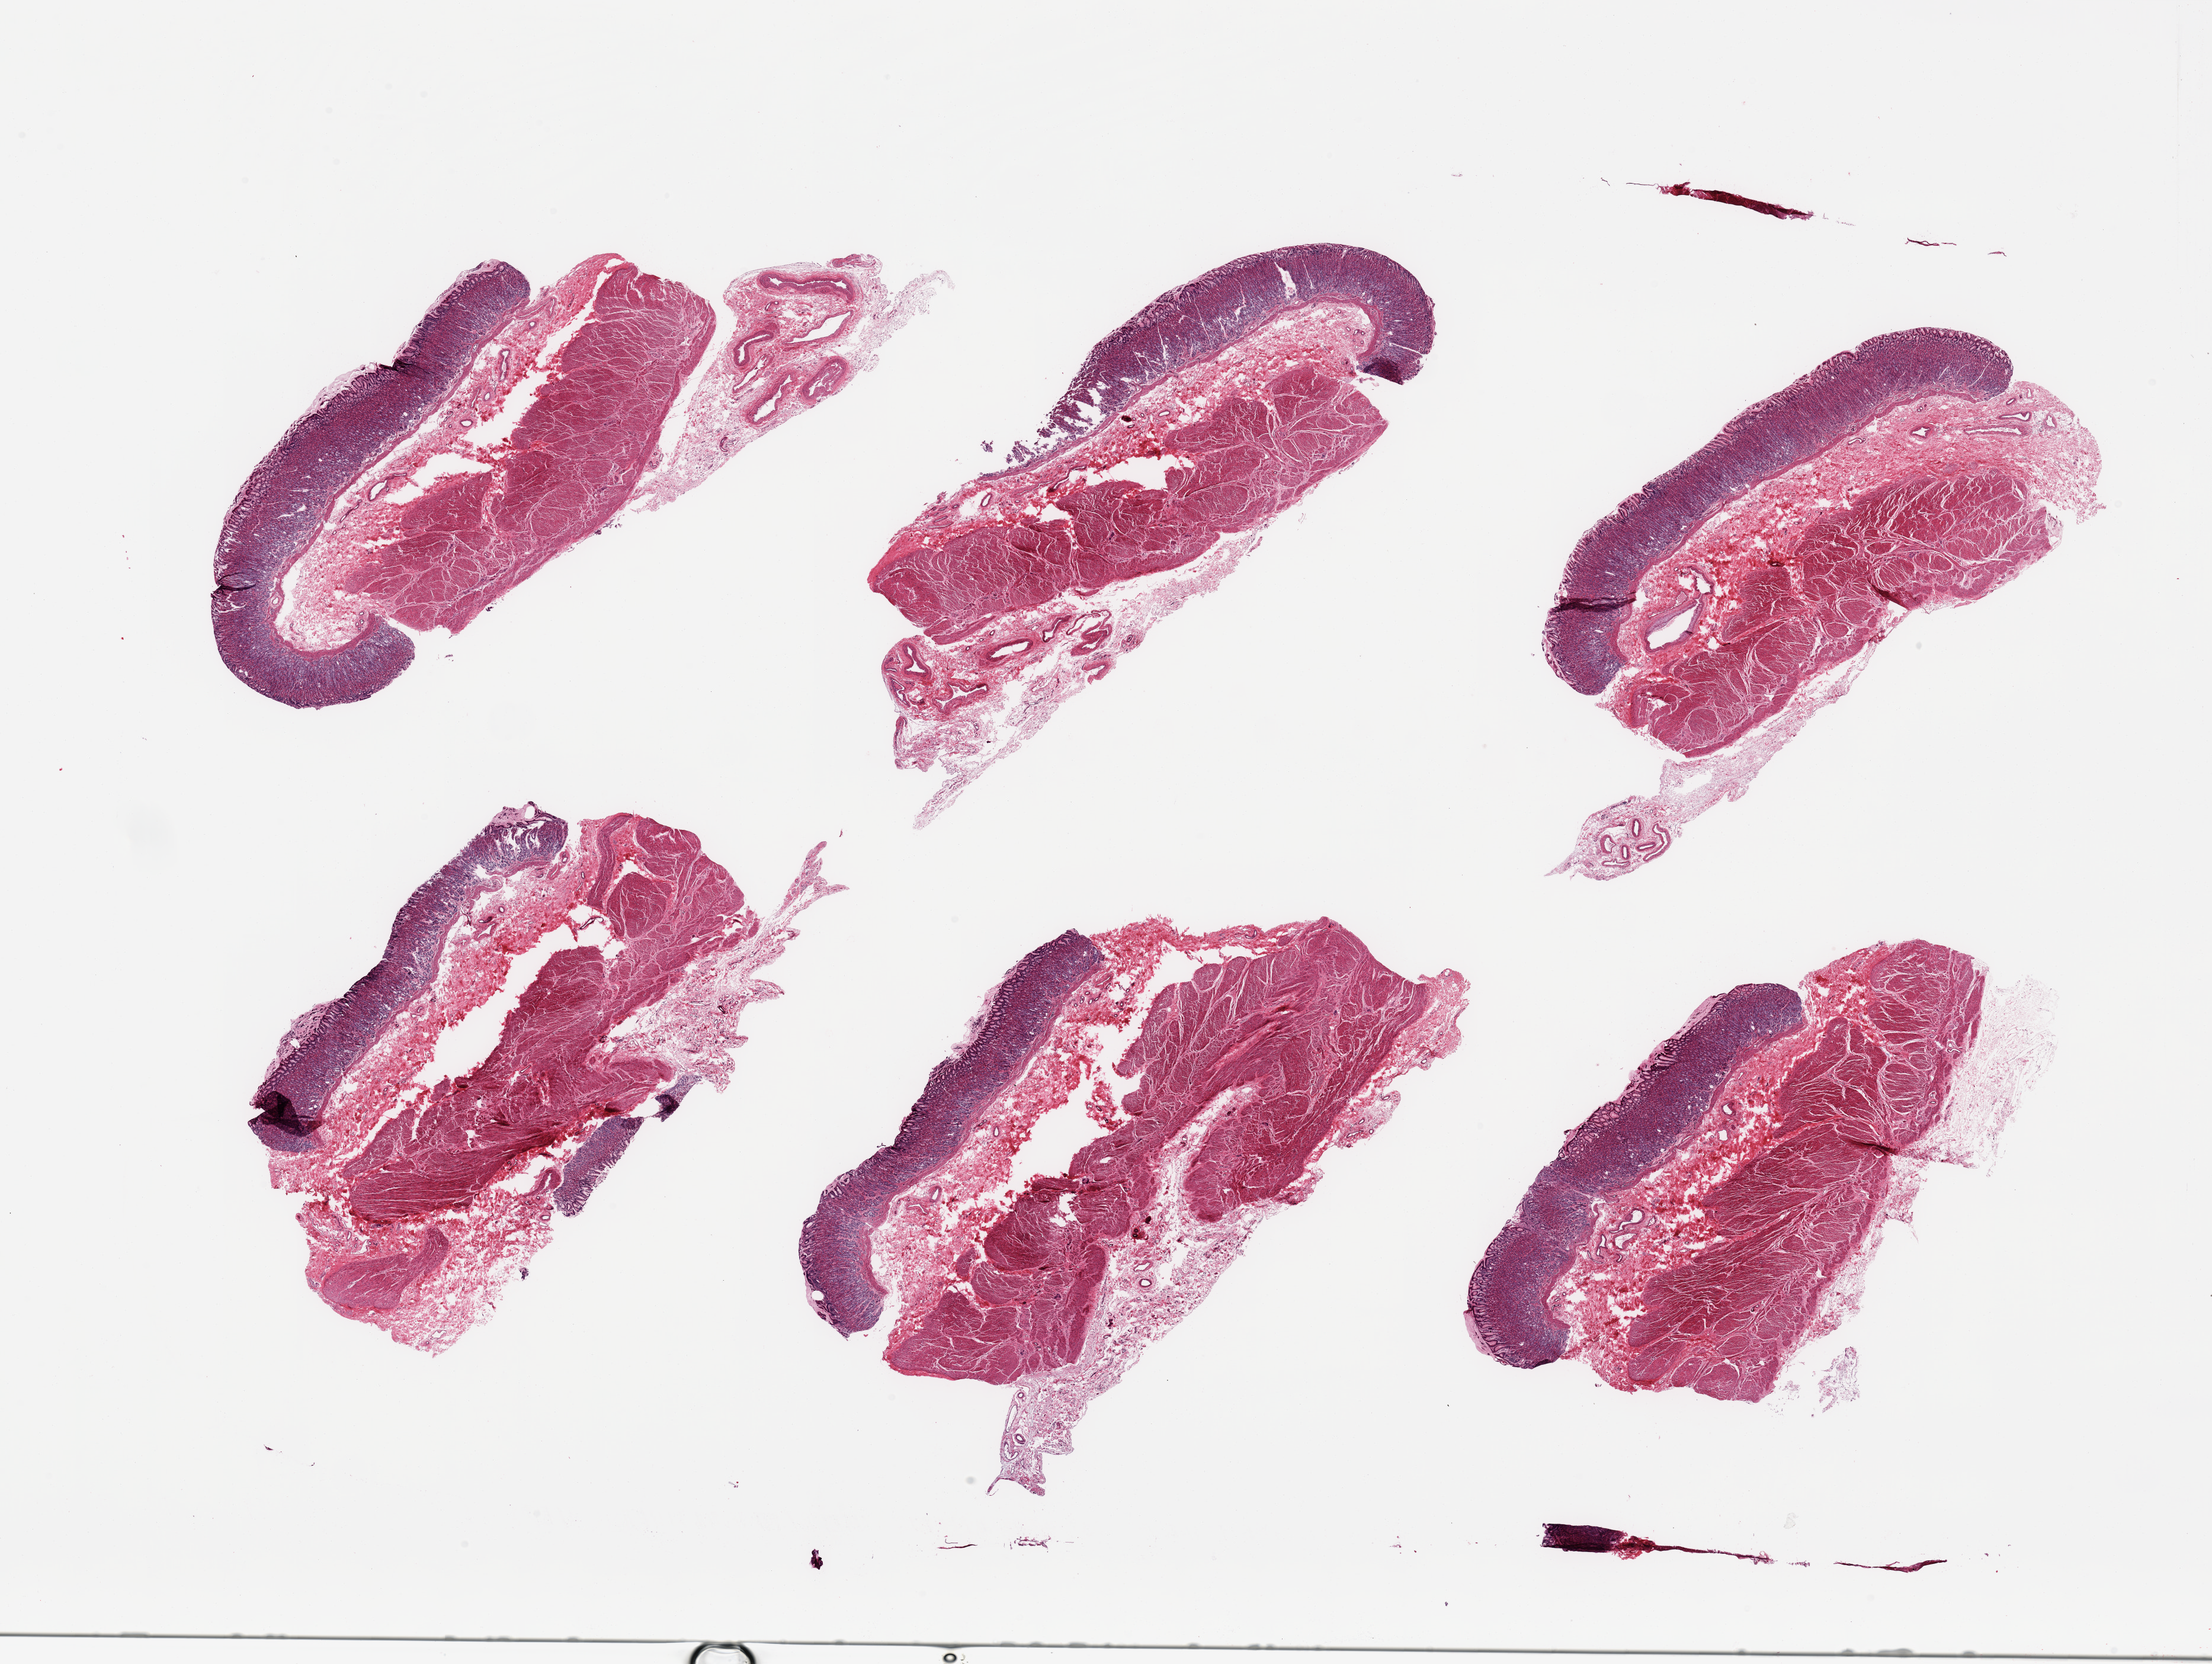
Whole-slide image, haematoxylin and eosin stain, low-resolution overview of the scanned area, about 29.5 x 22.2 mm; PAXgene-fixed paraffin-embedded (PFPE) section; sampled site (target tissue): stomach; tissue donor sample. Male donor.
Reviewer comment on this tissue sample: 6 pieces, mucosa up to ~0.7mm, ~20% of thickness; Focal mild microcystic metaplasia.